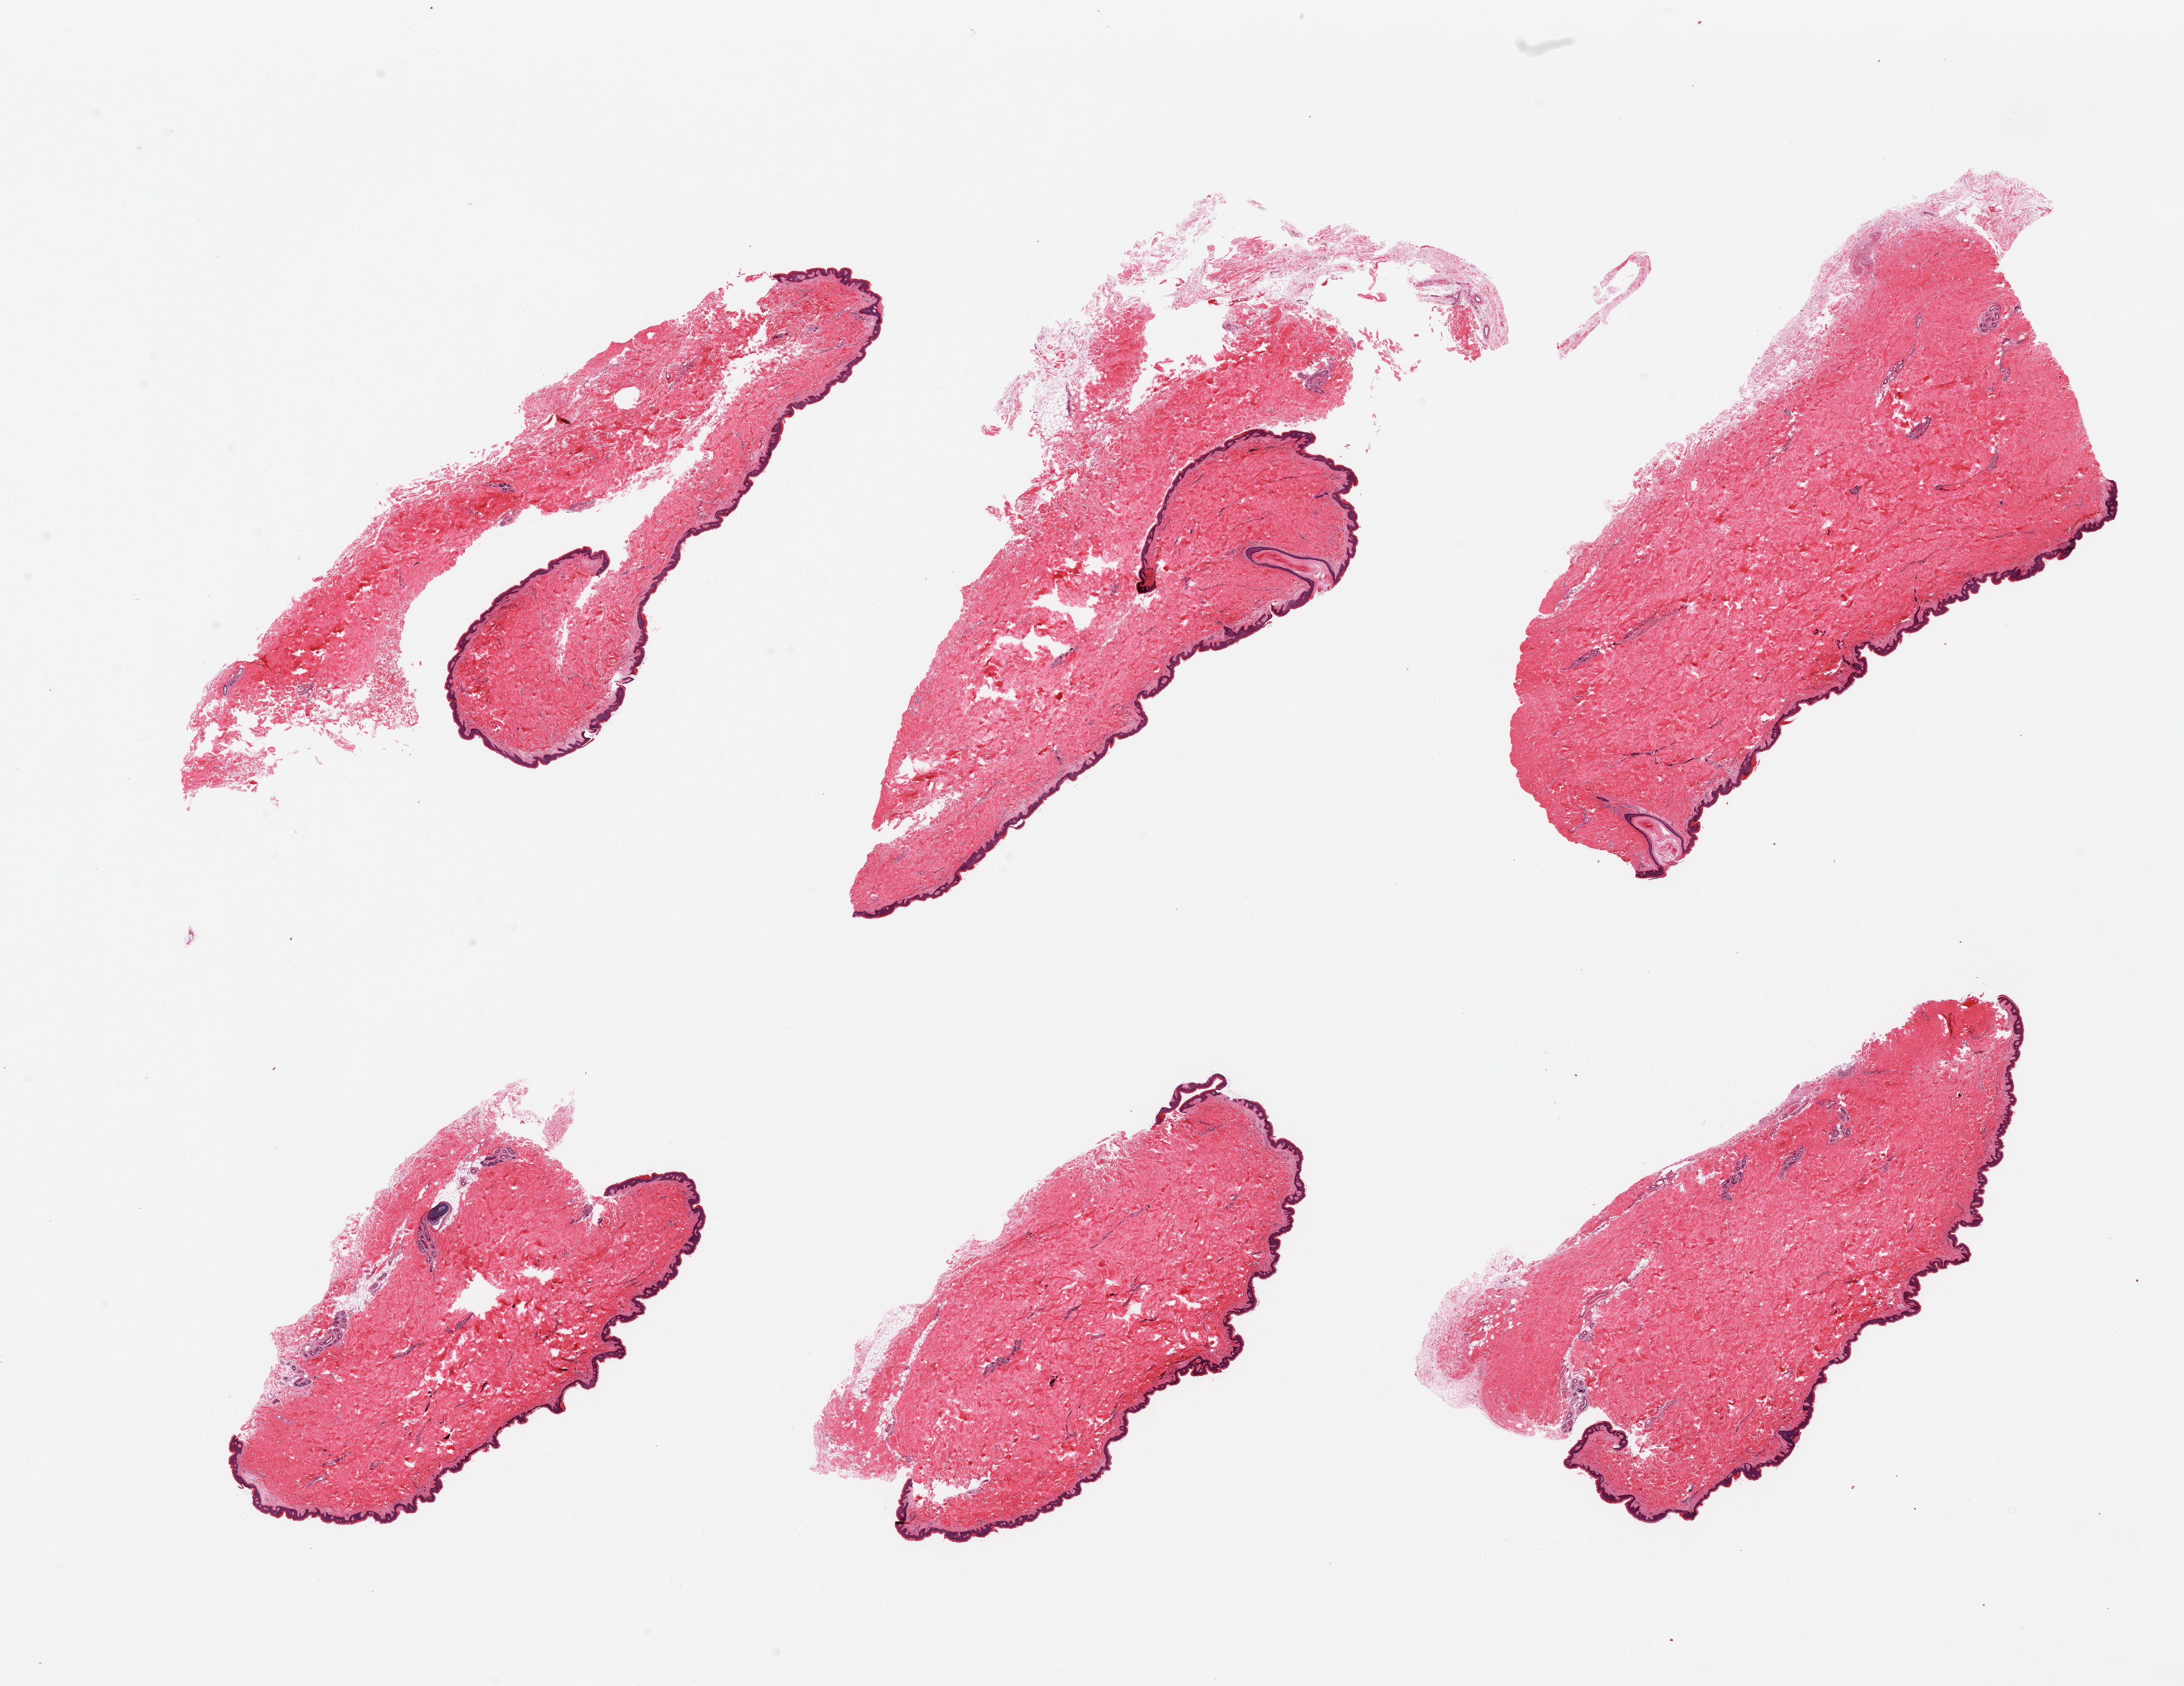
Digitized haematoxylin and eosin-stained section, brightfield, shown as a low-resolution overview of the whole scanned area (about 27.6 x 21.3 mm). PAXgene-fixed, paraffin-embedded tissue. Sampled site (target tissue): skin of suprapubic region. Tissue donor sample.
Pathologist's review note for this sample: 6 pieces, well trimmed.